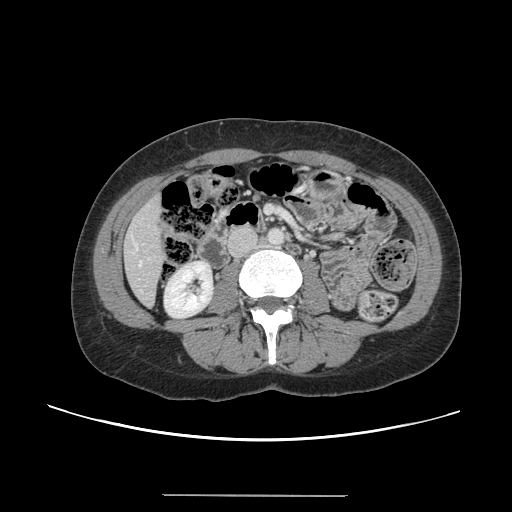
Contrast-enhanced abdominal CT, one axial slice; position 35 of 144 along the scan axis; intravenous contrast given; soft-tissue window (W 400 / L 40 HU); 2.5 mm slice thickness; 512 × 512 image matrix, field of view 380 × 380 mm. Female patient, age 53 years. From the clinical record (not read from this slice): diagnosis: colorectal cancer liver metastases, imaged before liver resection; multiple liver metastases: yes; largest metastasis: 1.1 cm; disease in both lobes: no.
Annotated regions visible in this slice (expert manual segmentation):
- hepatic veins: bounding box (x1, y1, x2, y2) in pixels: (136, 246, 142, 265)
- liver: (125, 197, 166, 305)
- planned liver remnant (the part of the liver to remain after resection): (125, 195, 165, 305)